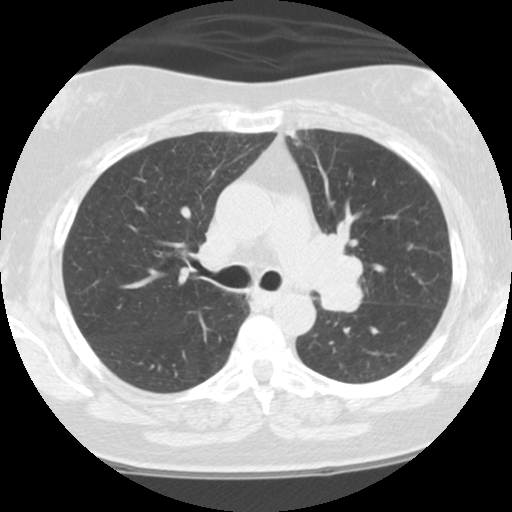
Low-dose screening chest CT, one axial slice. Position 71 of 108 along the scan axis. Reconstruction kernel STANDARD. Lung window (W 1500 / L -600 HU). 512 × 512 image matrix.
Annotated regions visible in this slice (manually delineated by an expert):
- lesion 1 (tumor, hilum of left lung): box from (x=293, y=236) to (x=363, y=312) px